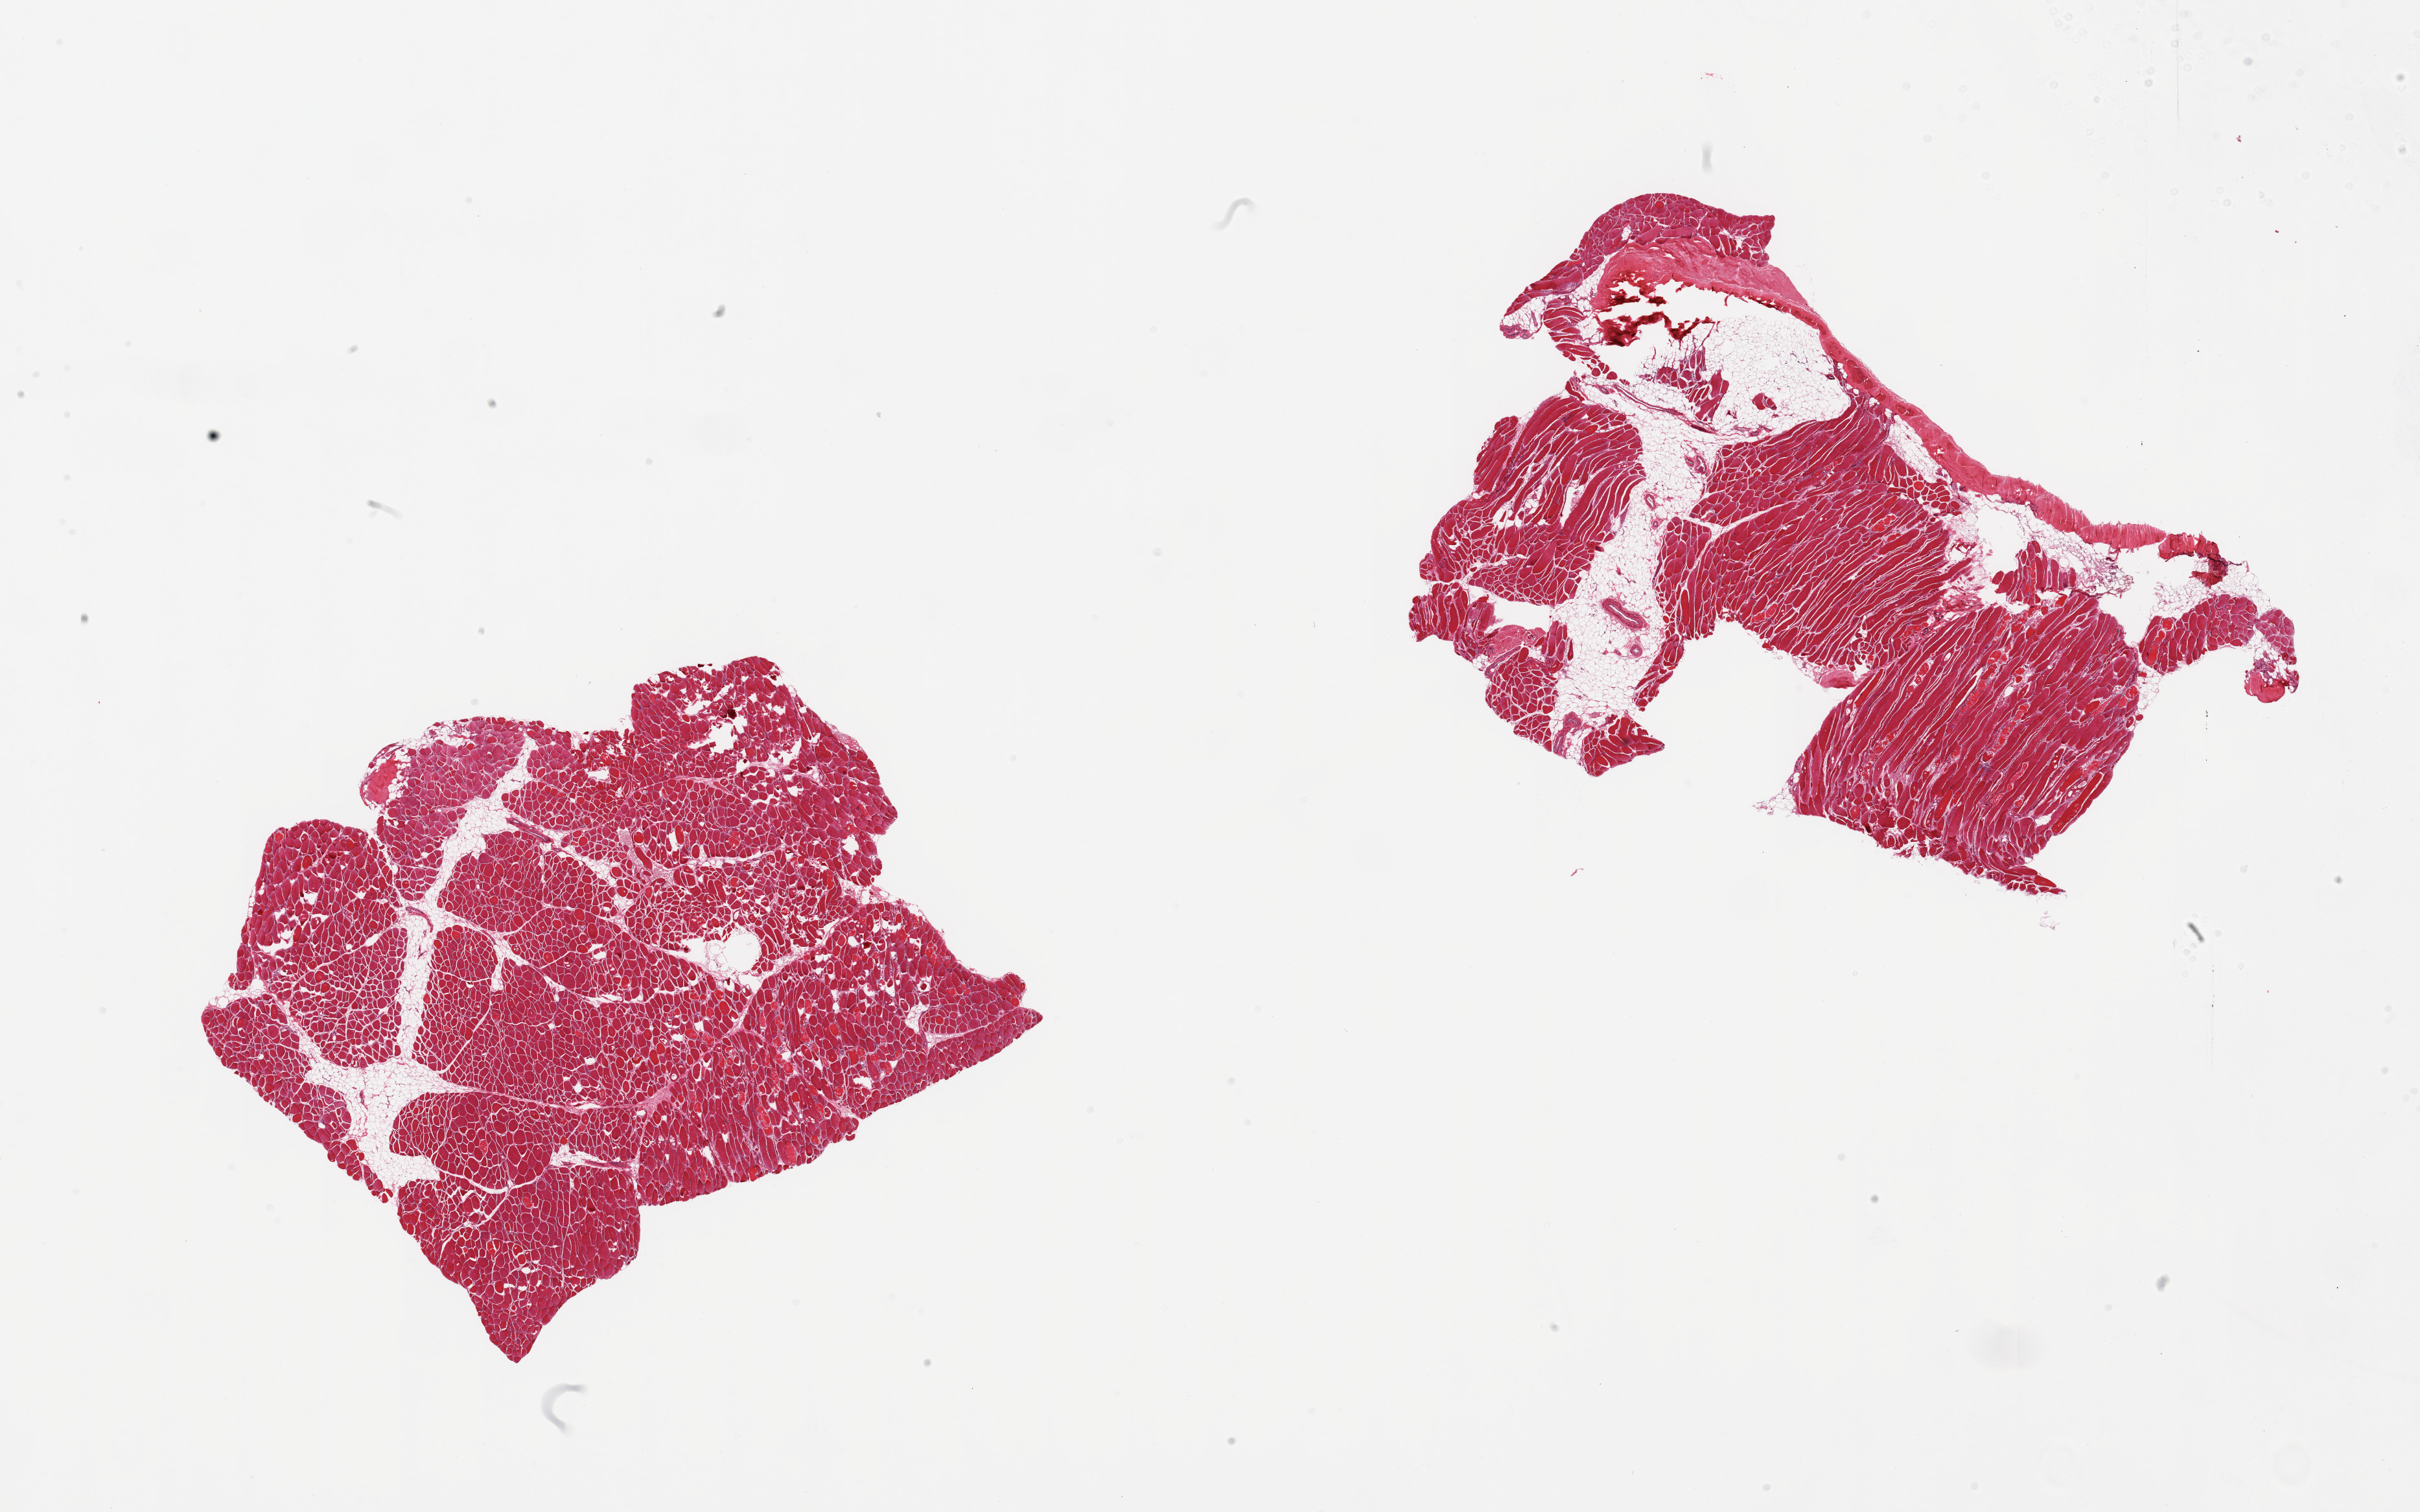
Digitized haematoxylin and eosin-stained section, brightfield — shown as a low-resolution overview of the whole scanned area (about 29.5 x 18.5 mm); PAXgene-fixed, paraffin-embedded tissue; target tissue: skeletal muscle; donor tissue sample. Donor sex: male.
Reviewer comment on this tissue sample: 2 pieces; one is 10% internal fat, second includes 20-30 fat and tendon, scattered atrophic fibers, interspersed degenerating myocytes c/w rhabdomyolysis.